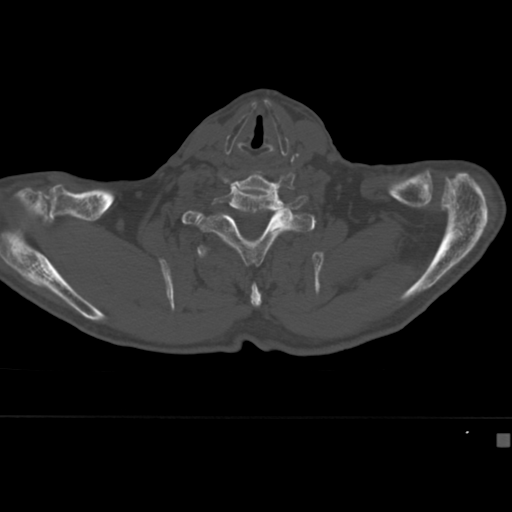
CT including the spine, one axial slice; slice 354 of 430 in the series (ordered by position); 120 kVp; bone window (W 1800 / L 400 HU); 512 × 512 image matrix. Patient: male, 64 years. Case-level facts recorded for this patient, not image findings: primary cancer: uterus; vertebrae with lytic lesions (as recorded): T1, T4, T5, T7, L5.
Outlined on this slice (semi-automatically segmented with operator editing):
- T2 vertebra: bounding box (x1, y1, x2, y2) in pixels: (197, 244, 262, 308)